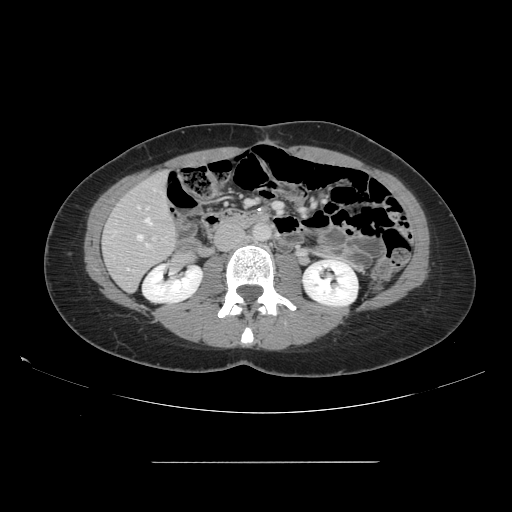
Contrast-enhanced abdominal CT, one axial slice; position 51 of 151 along the scan axis; 120 kVp; soft-tissue window (W 400 / L 40 HU); 2.5 mm slice thickness; 512 × 512 image matrix. Female patient, age 46 years. Case-level facts recorded for this patient, not image findings: diagnosis: colorectal cancer liver metastases, imaged before liver resection; multiple liver metastases: yes.
Structures marked on this image (outlined manually by an expert reader):
- hepatic veins: bounding box [x1, y1, x2, y2] px = [137, 218, 152, 240]
- liver: [104, 173, 177, 291]
- planned liver remnant (the part of the liver to remain after resection): [104, 174, 177, 291]